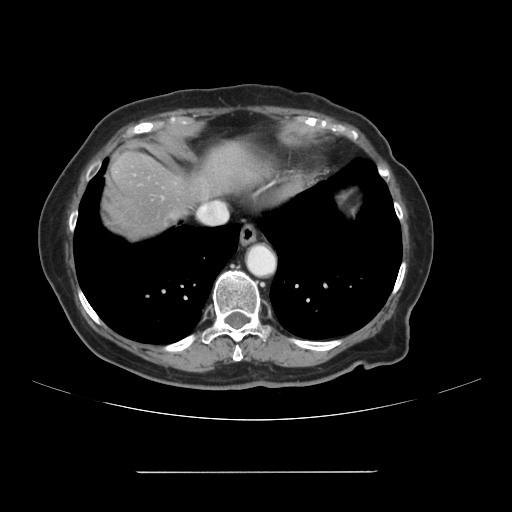
Contrast-enhanced abdominal CT, one axial slice. Position 100 of 111 along the scan axis. Intravenous contrast given. Soft-tissue window (W 400 / L 40 HU). 2.5 mm slice thickness. 512 × 512 image matrix, field of view 400 × 400 mm. Female patient, age 74 years. Case-level facts recorded for this patient, not image findings: diagnosis: colorectal cancer liver metastases, imaged before liver resection; multiple liver metastases: yes; largest metastasis: 1.1 cm.
Annotated regions visible in this slice (manually delineated by an expert):
- liver: bounding box <102,141,266,242> (left, top, right, bottom; pixels)
- planned liver remnant (the part of the liver to remain after resection): <204,141,266,193>
- liver metastasis: <167,216,175,225>